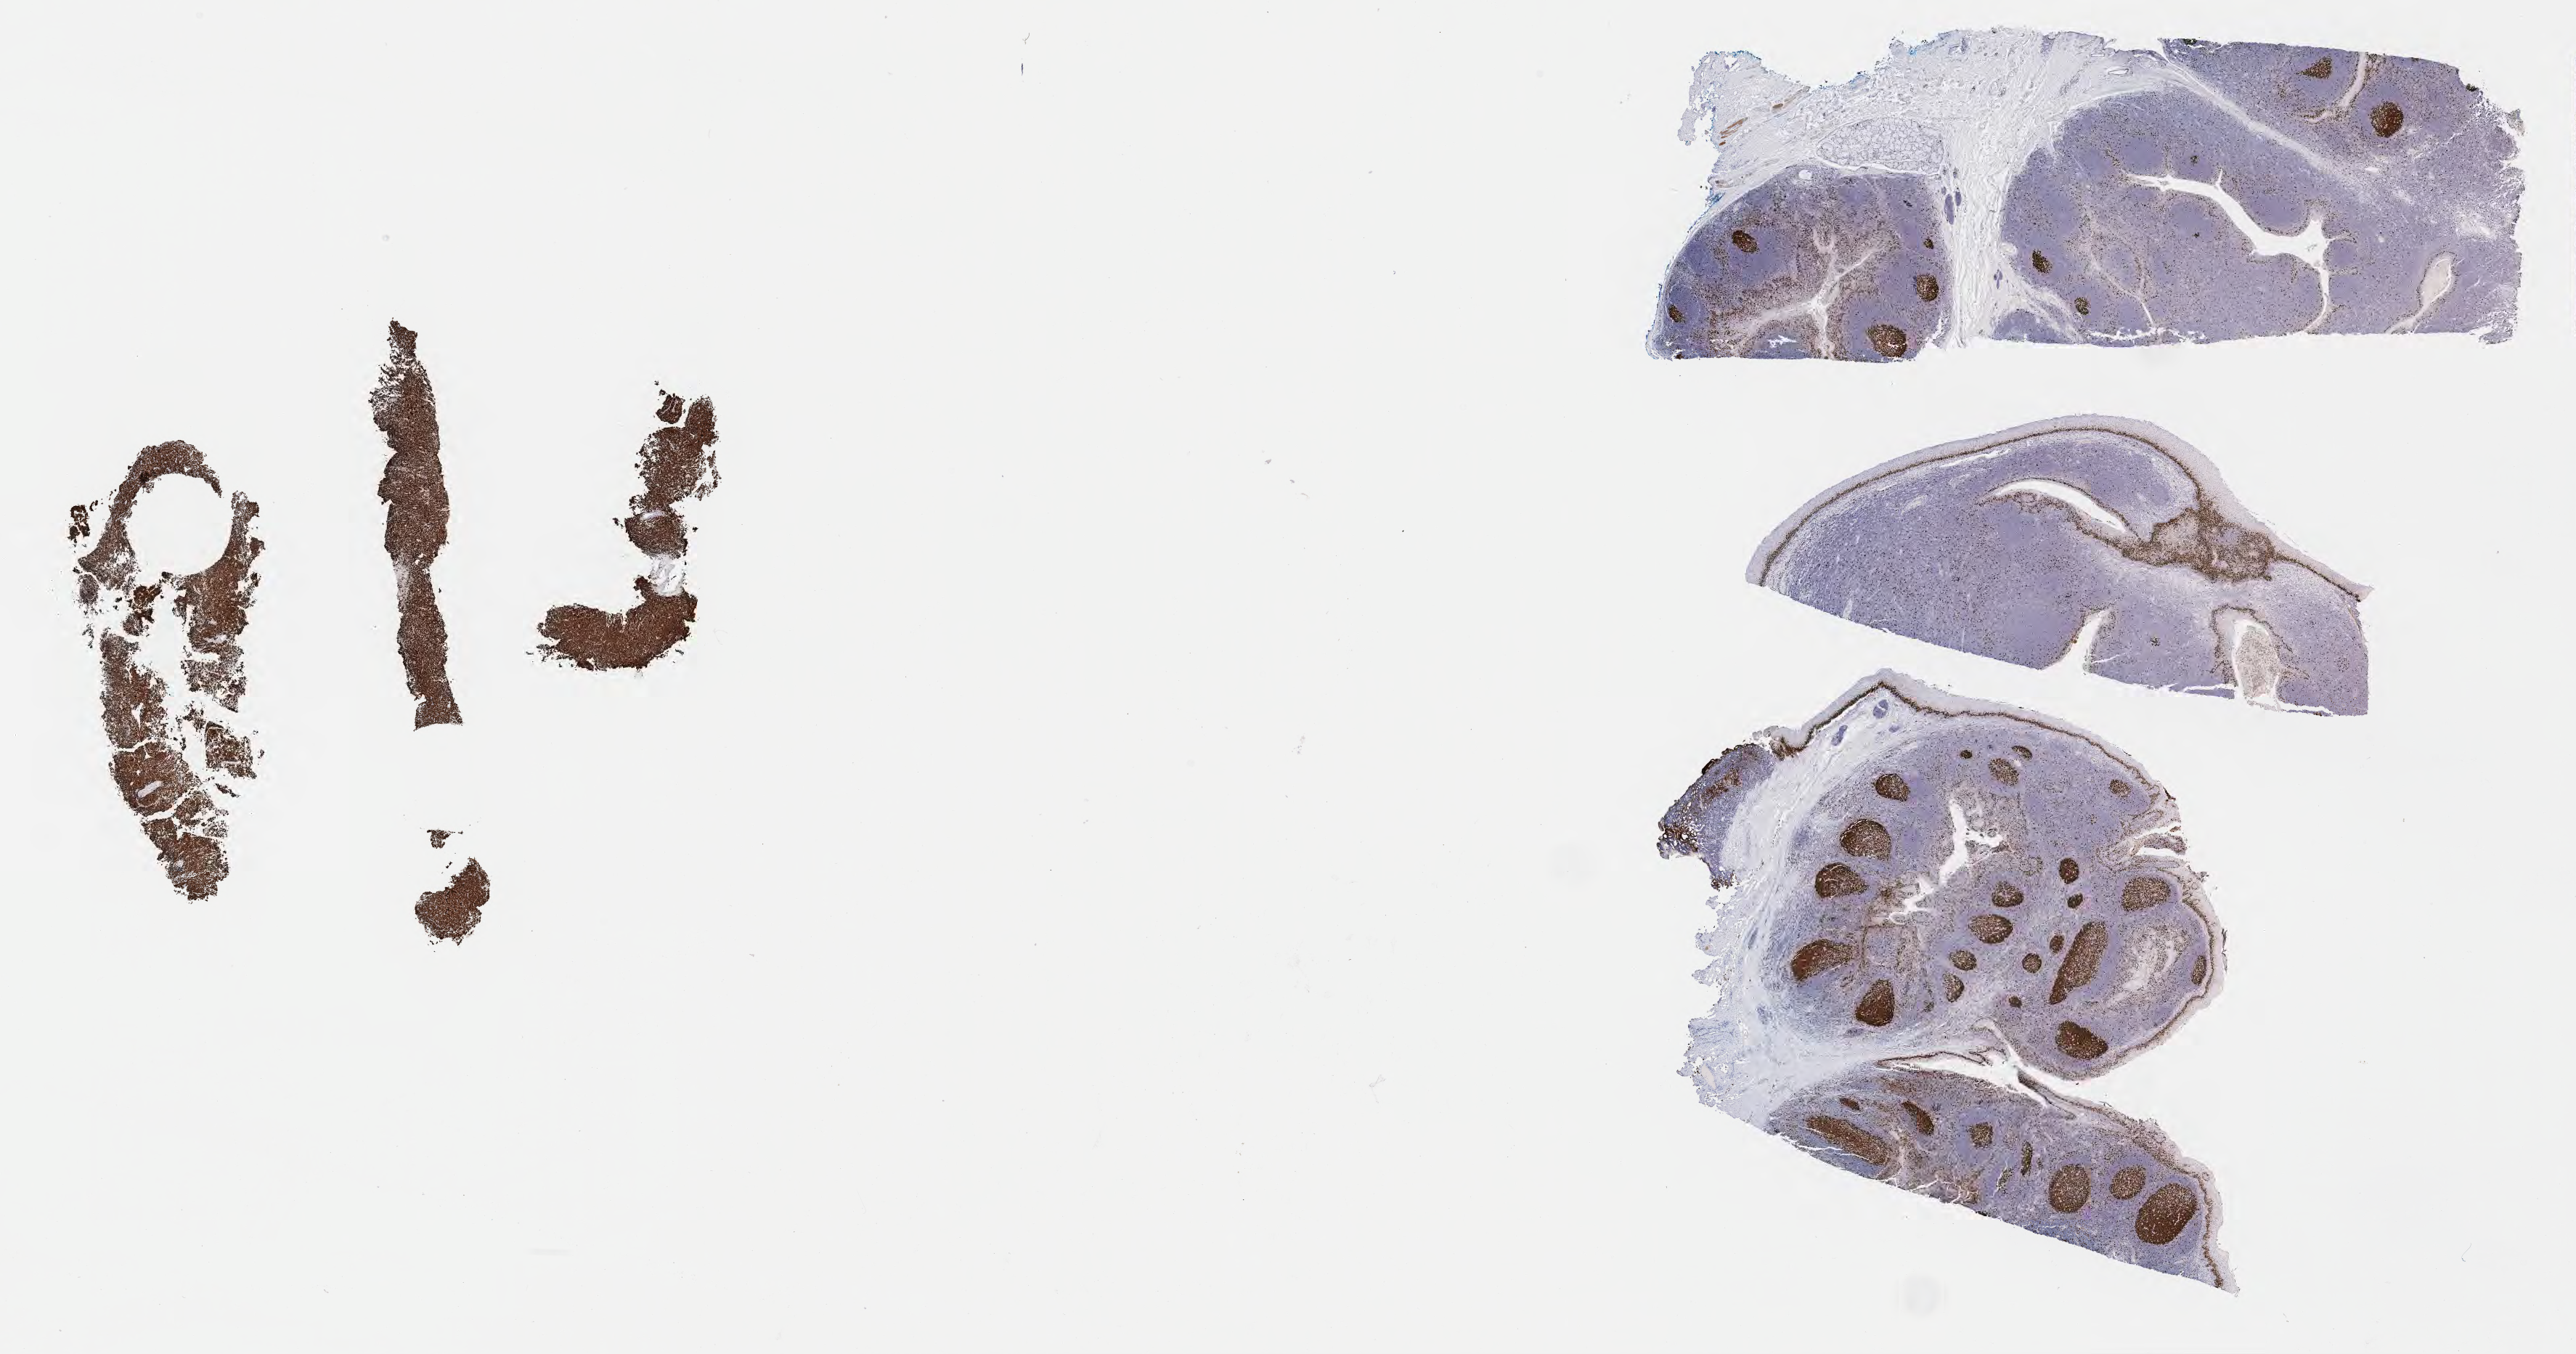
IHC for Ki-67, whole-slide image, whole scanned area (about 28.7 x 15.1 mm) shown as a low-resolution overview. Tumor tissue. Site: spleen. Male, age 8 years at initial diagnosis.
- histologic diagnosis: Burkitt lymphoma, NOS